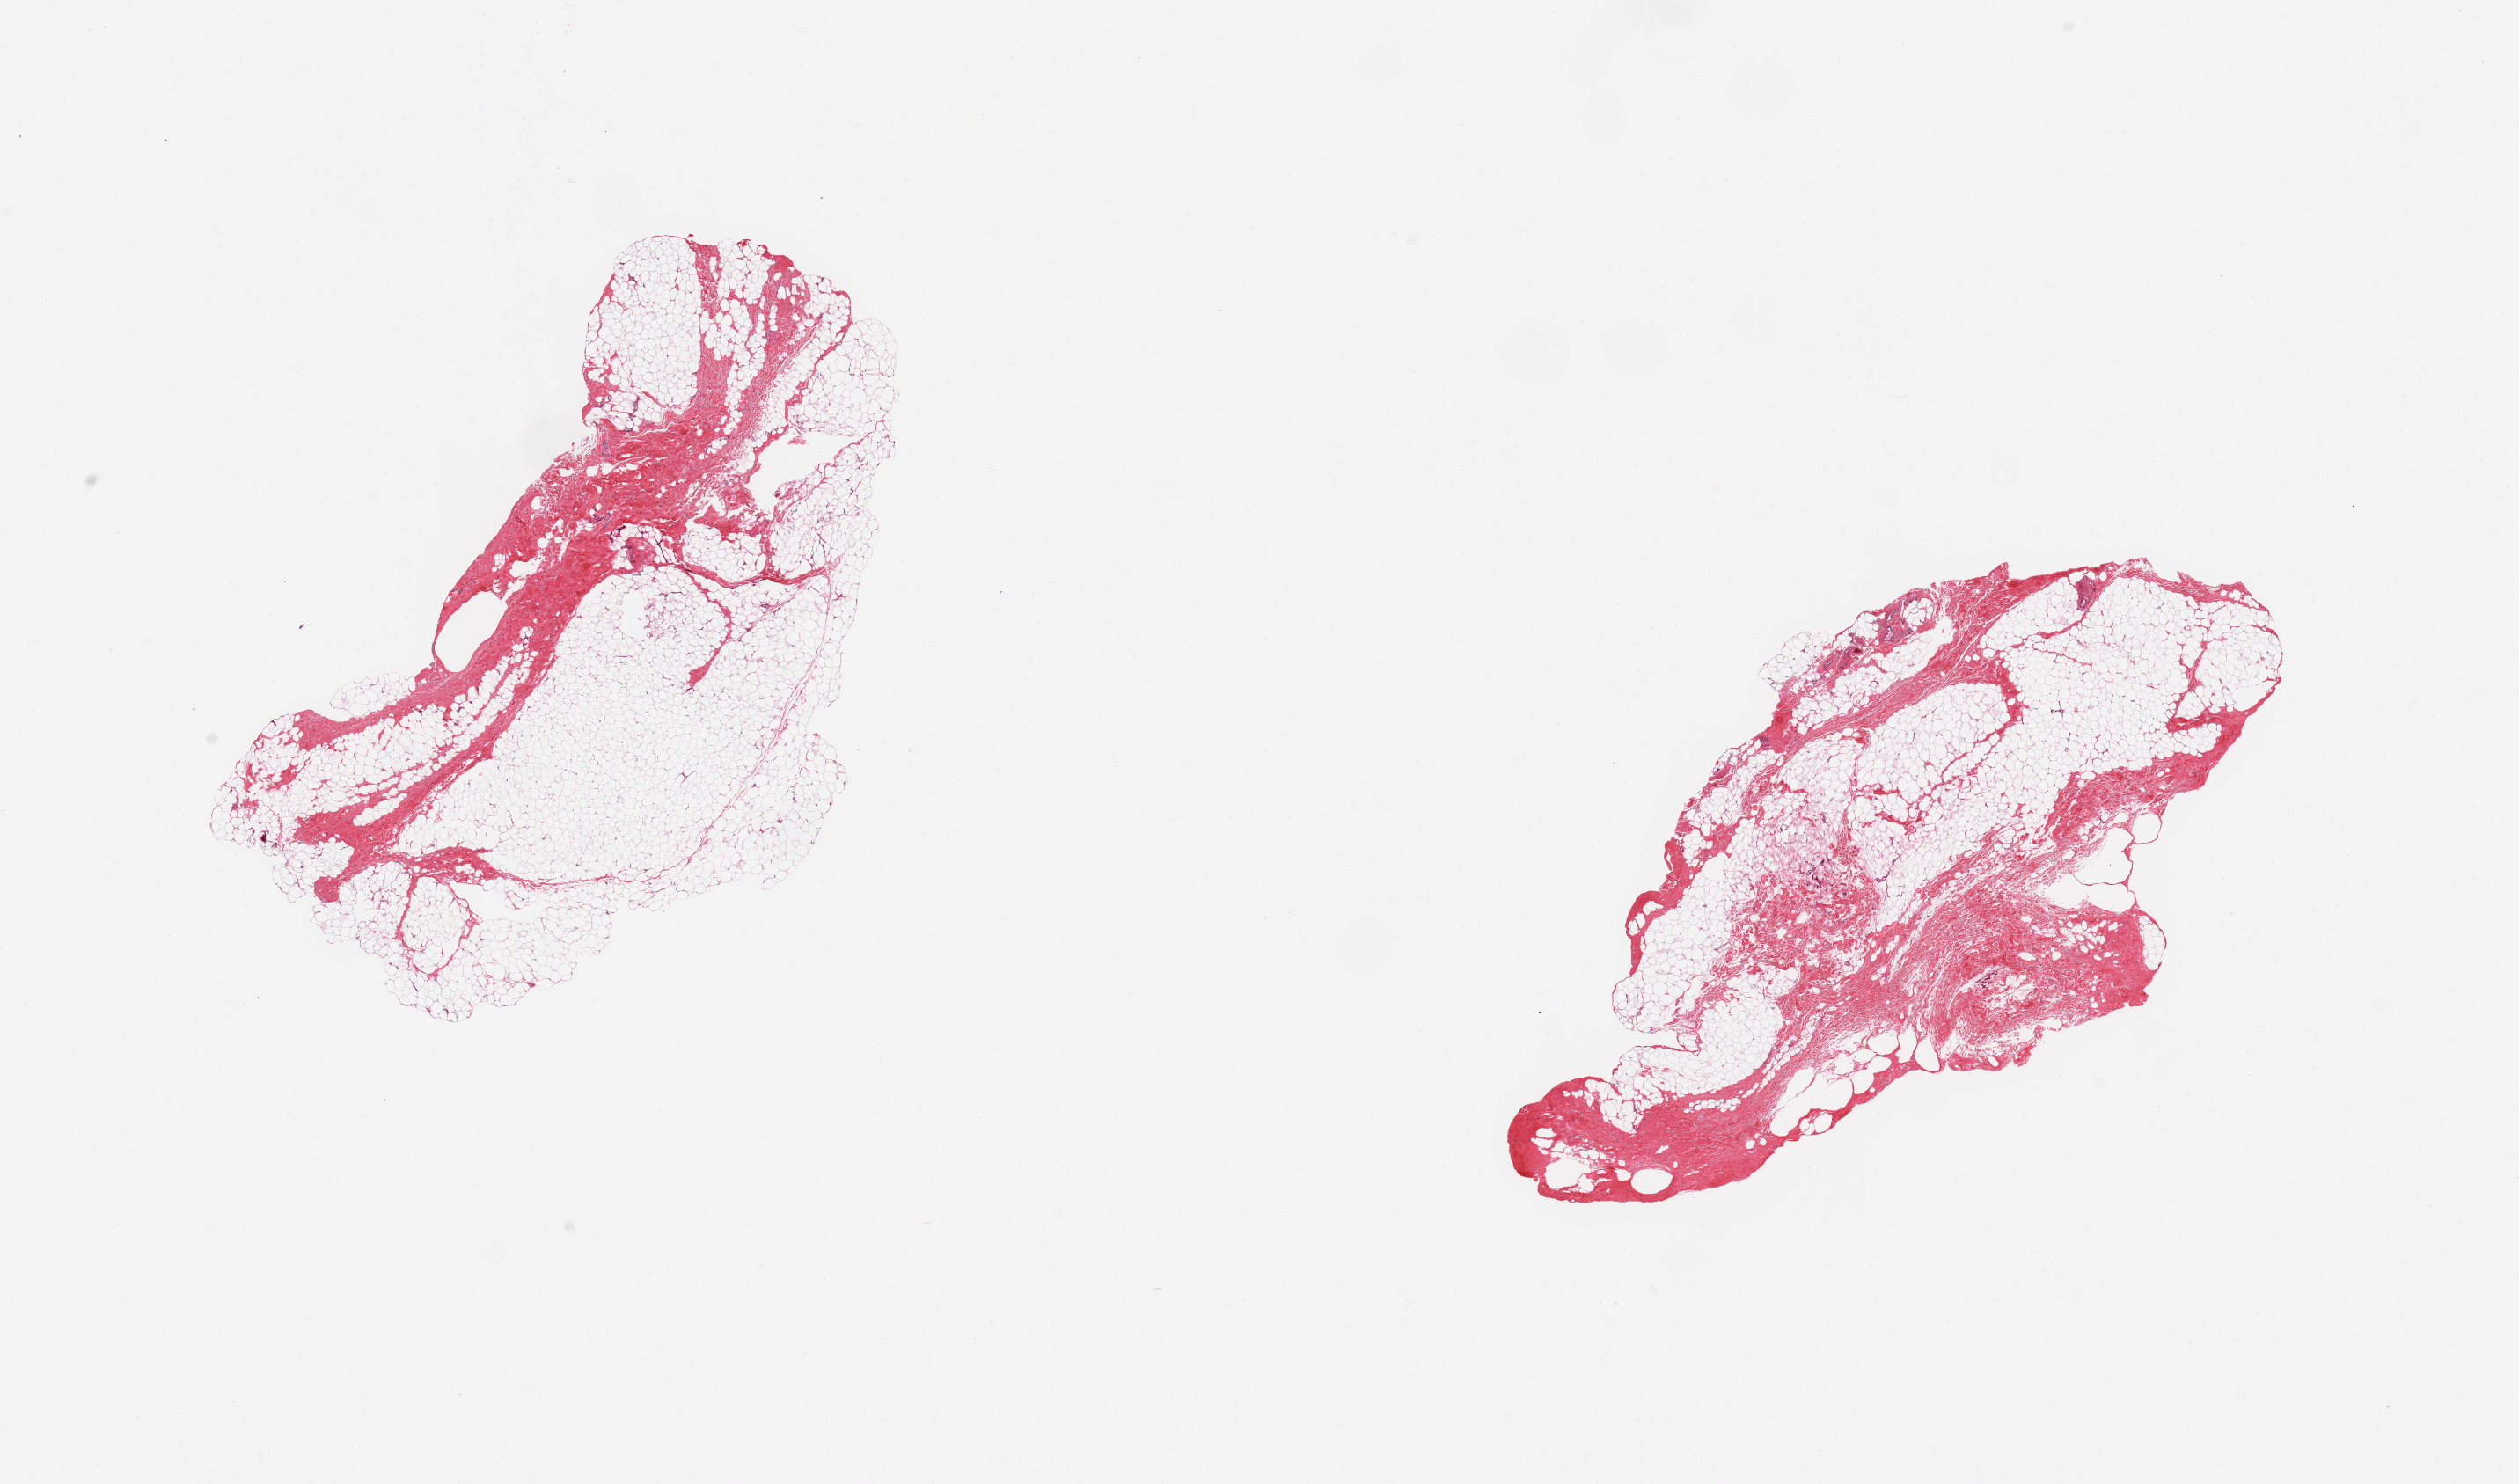
Digitized haematoxylin and eosin-stained section, shown as a low-resolution overview of the whole scanned area (about 22.6 x 13.3 mm); PAXgene-fixed, paraffin-embedded tissue; target tissue: breast; tissue donor sample.
Pathologist's review note for this sample: 2 pieces; predominantly fat with 15-40% stroma, no ductal elements in this section.